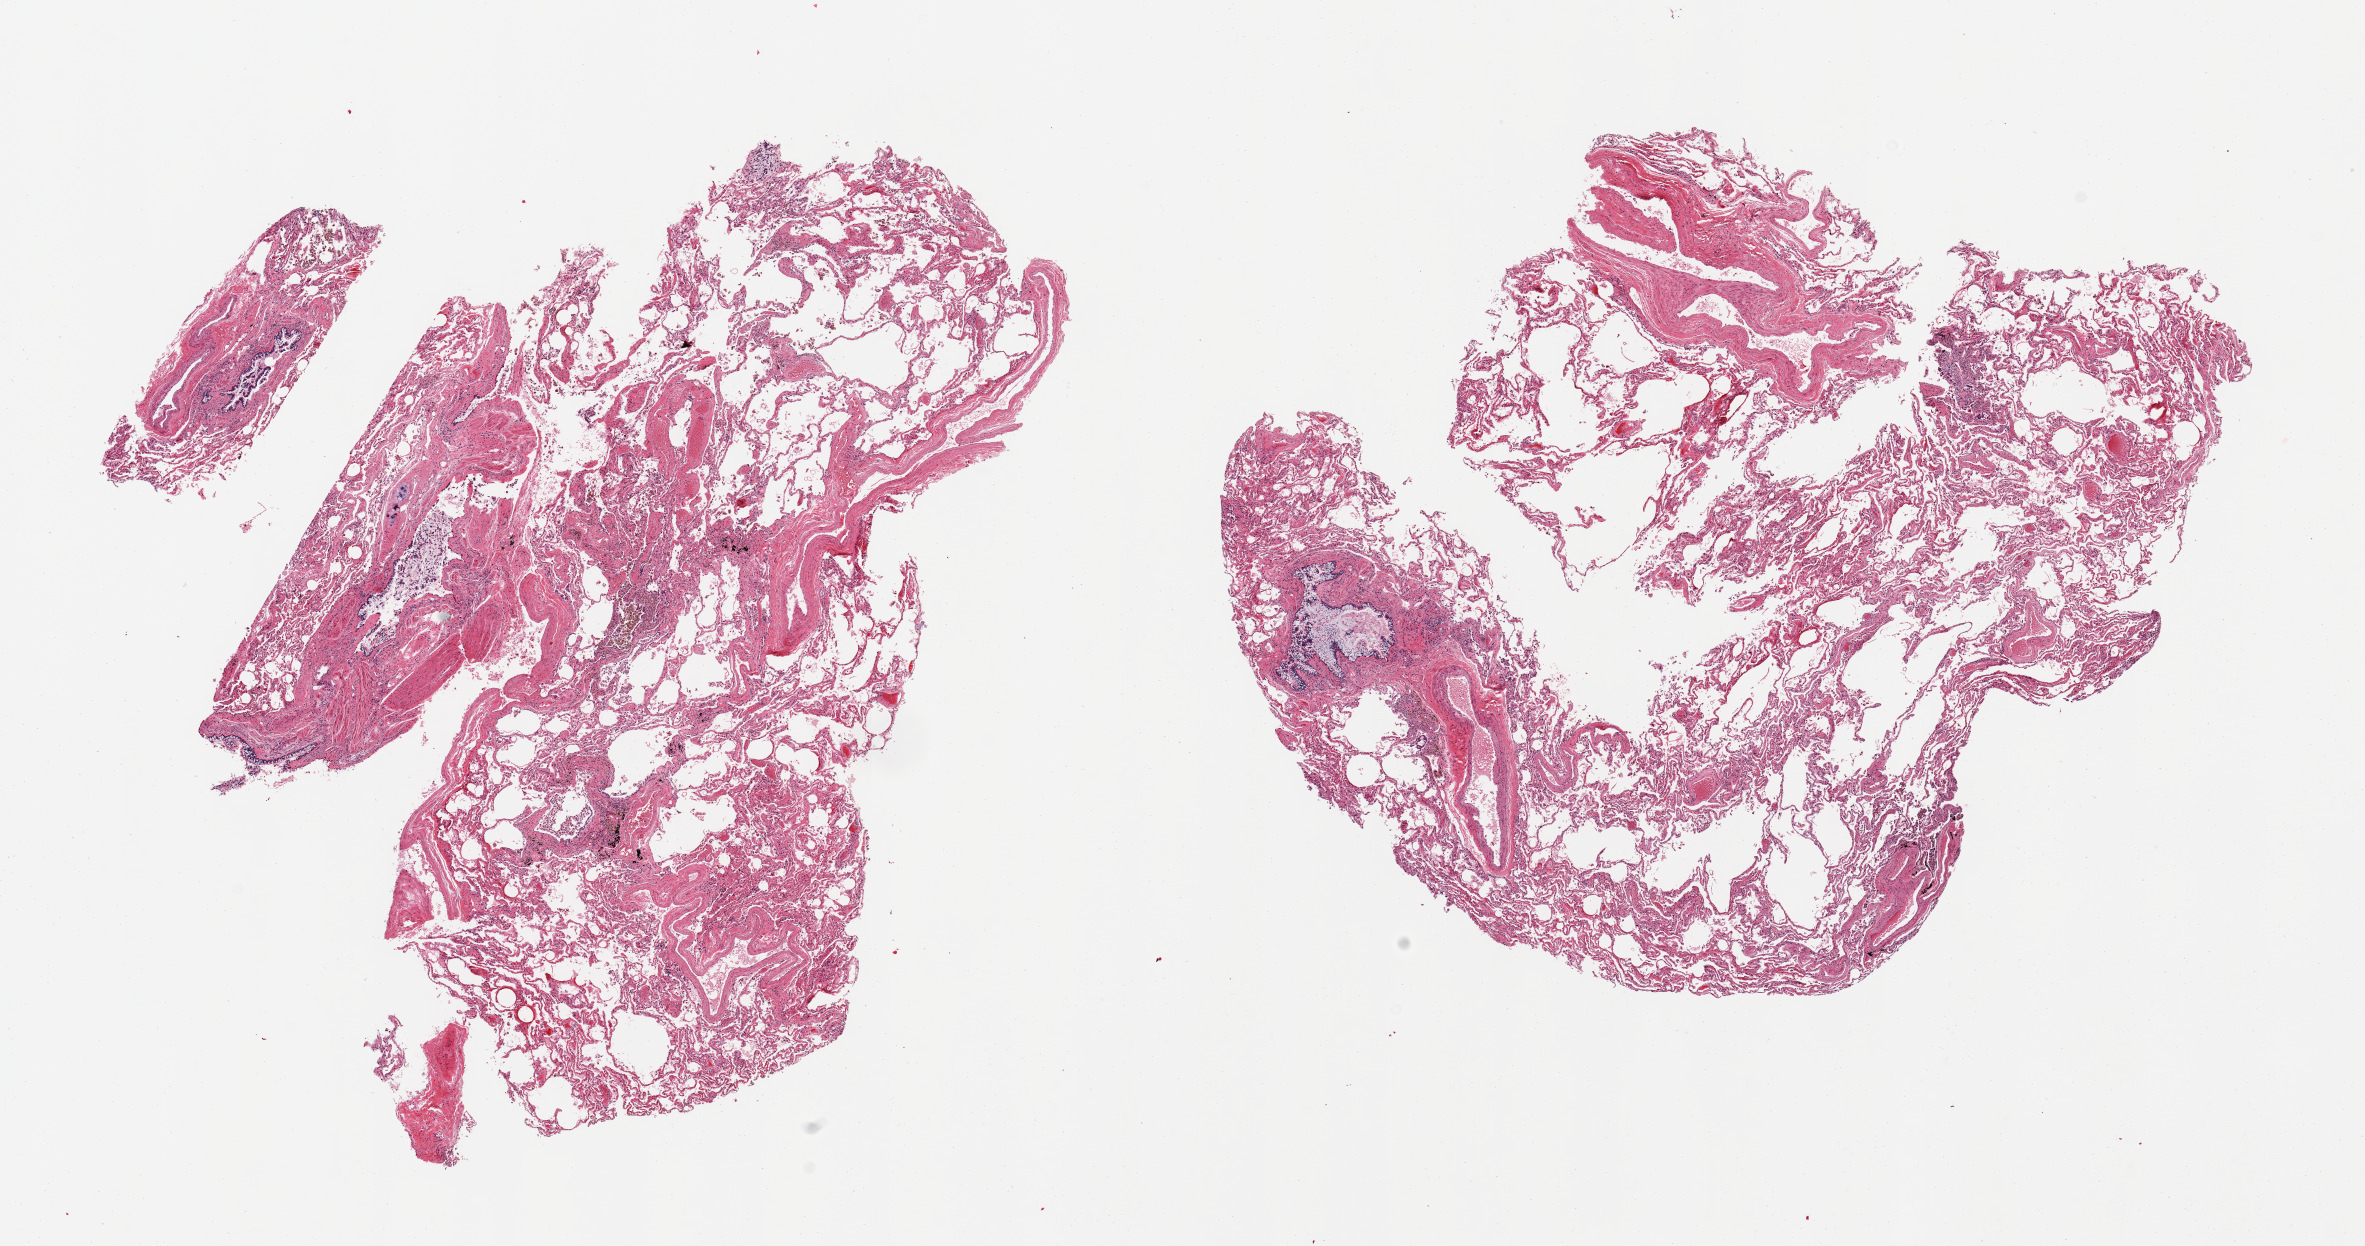
Digitized haematoxylin and eosin-stained section — a low-resolution overview of the entire scanned area, about 18.7 x 9.9 mm, PAXgene-fixed, paraffin-embedded tissue, target tissue: lung, tissue donor sample. Donor sex: male.
Pathologist's review note for this sample: 2 pieces; emphysema; pigmented alveolar macrophages.